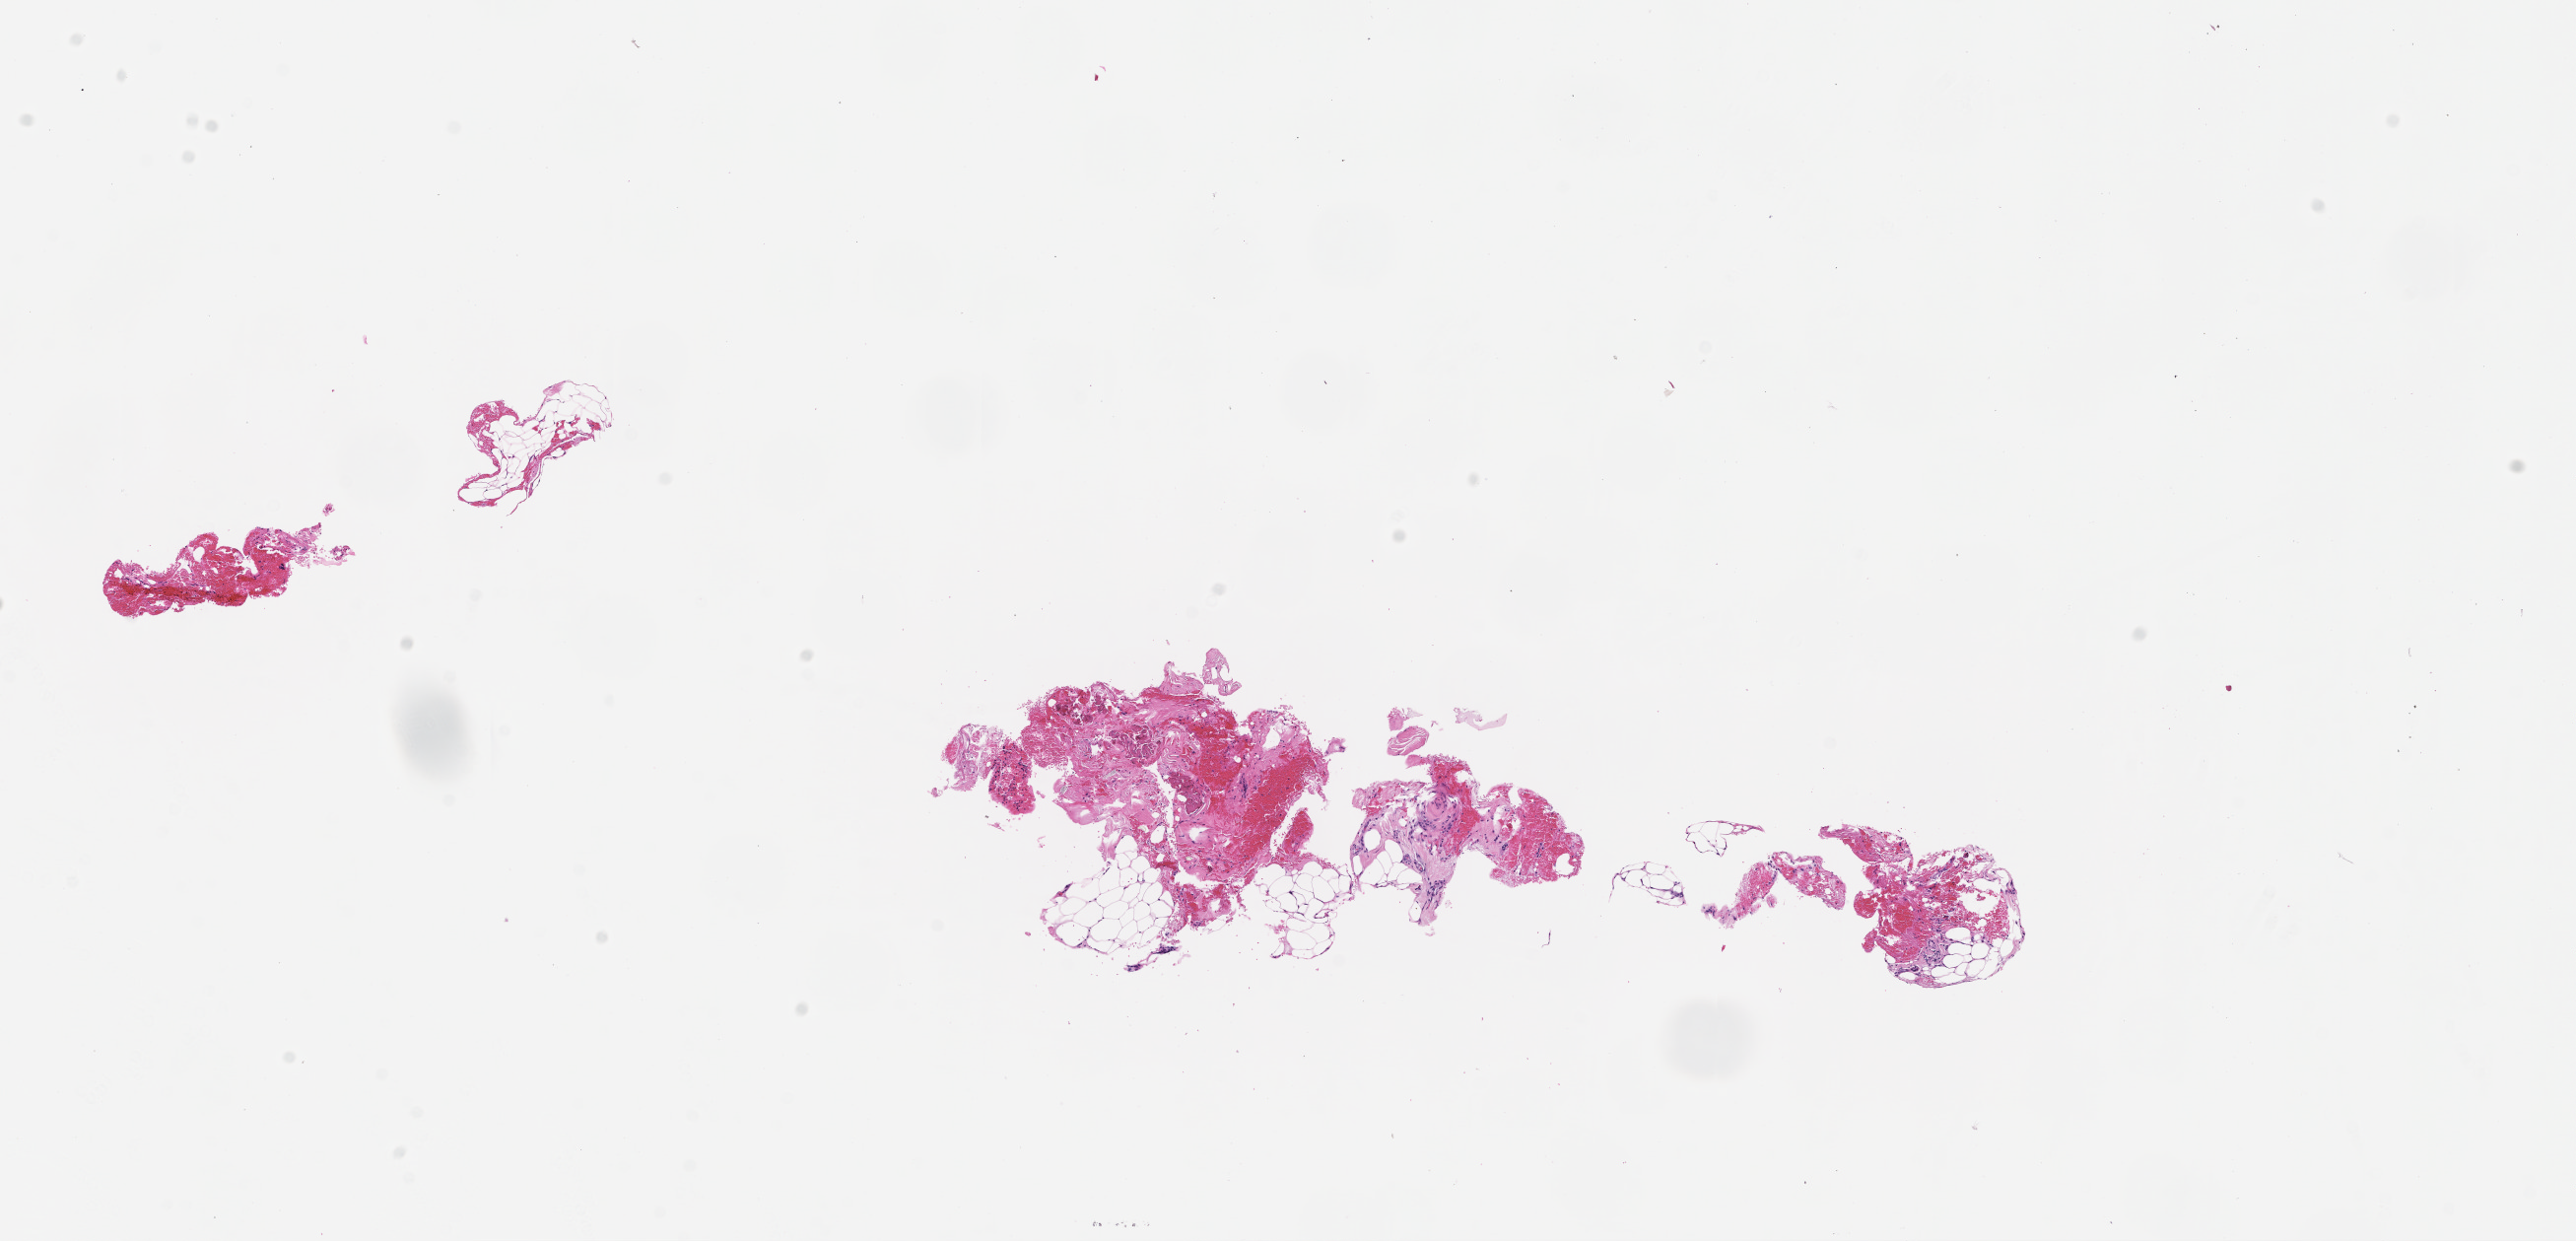
Whole-slide image, haematoxylin and eosin stain — whole scanned area (about 10.6 x 5.1 mm) shown as a low-resolution overview, FFPE section. Patient sex: female.
- this section: metastatic tumor tissue
- patient diagnosis (primary): Colorectal Carcinoma